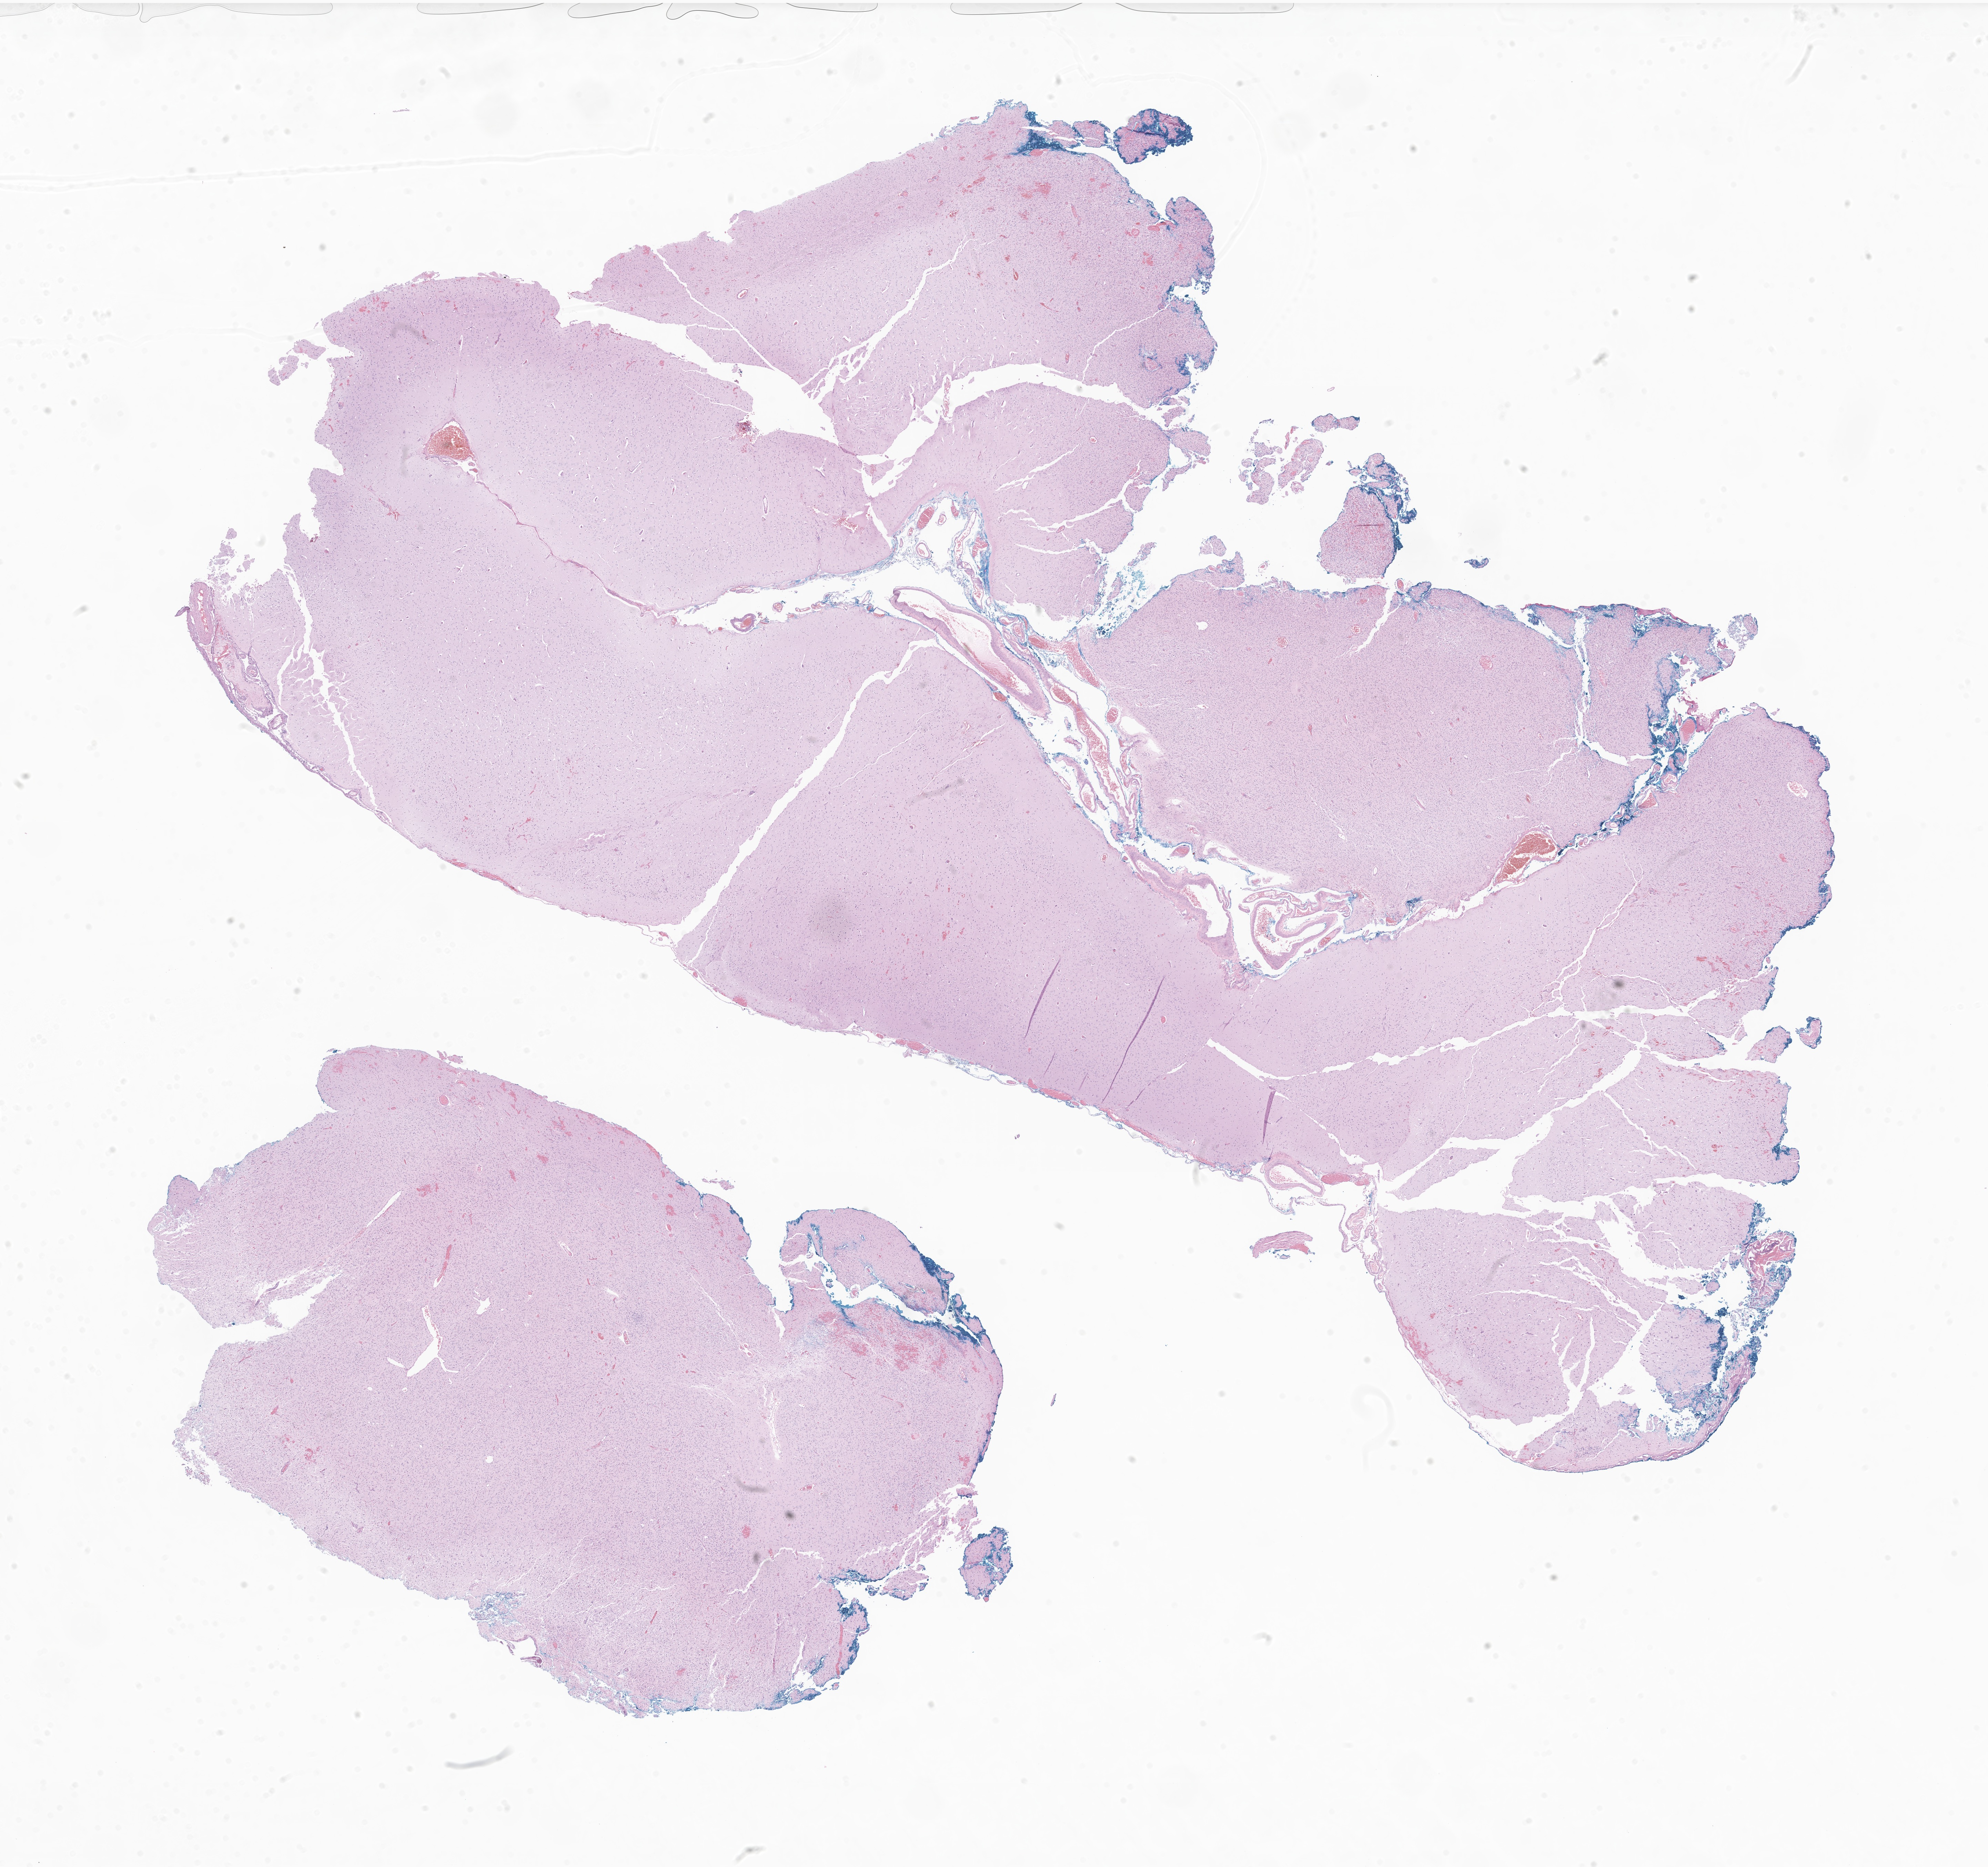
Digitized haematoxylin and eosin-stained section of tumor tissue from the temporal lobe — whole scanned area (about 24.3 x 22.8 mm) shown as a low-resolution overview, formalin-fixed paraffin-embedded section. Patient: female, age 178 months (14 years 10 months).
Diagnosis: Dysembryoplastic neuroepithelial tumor.